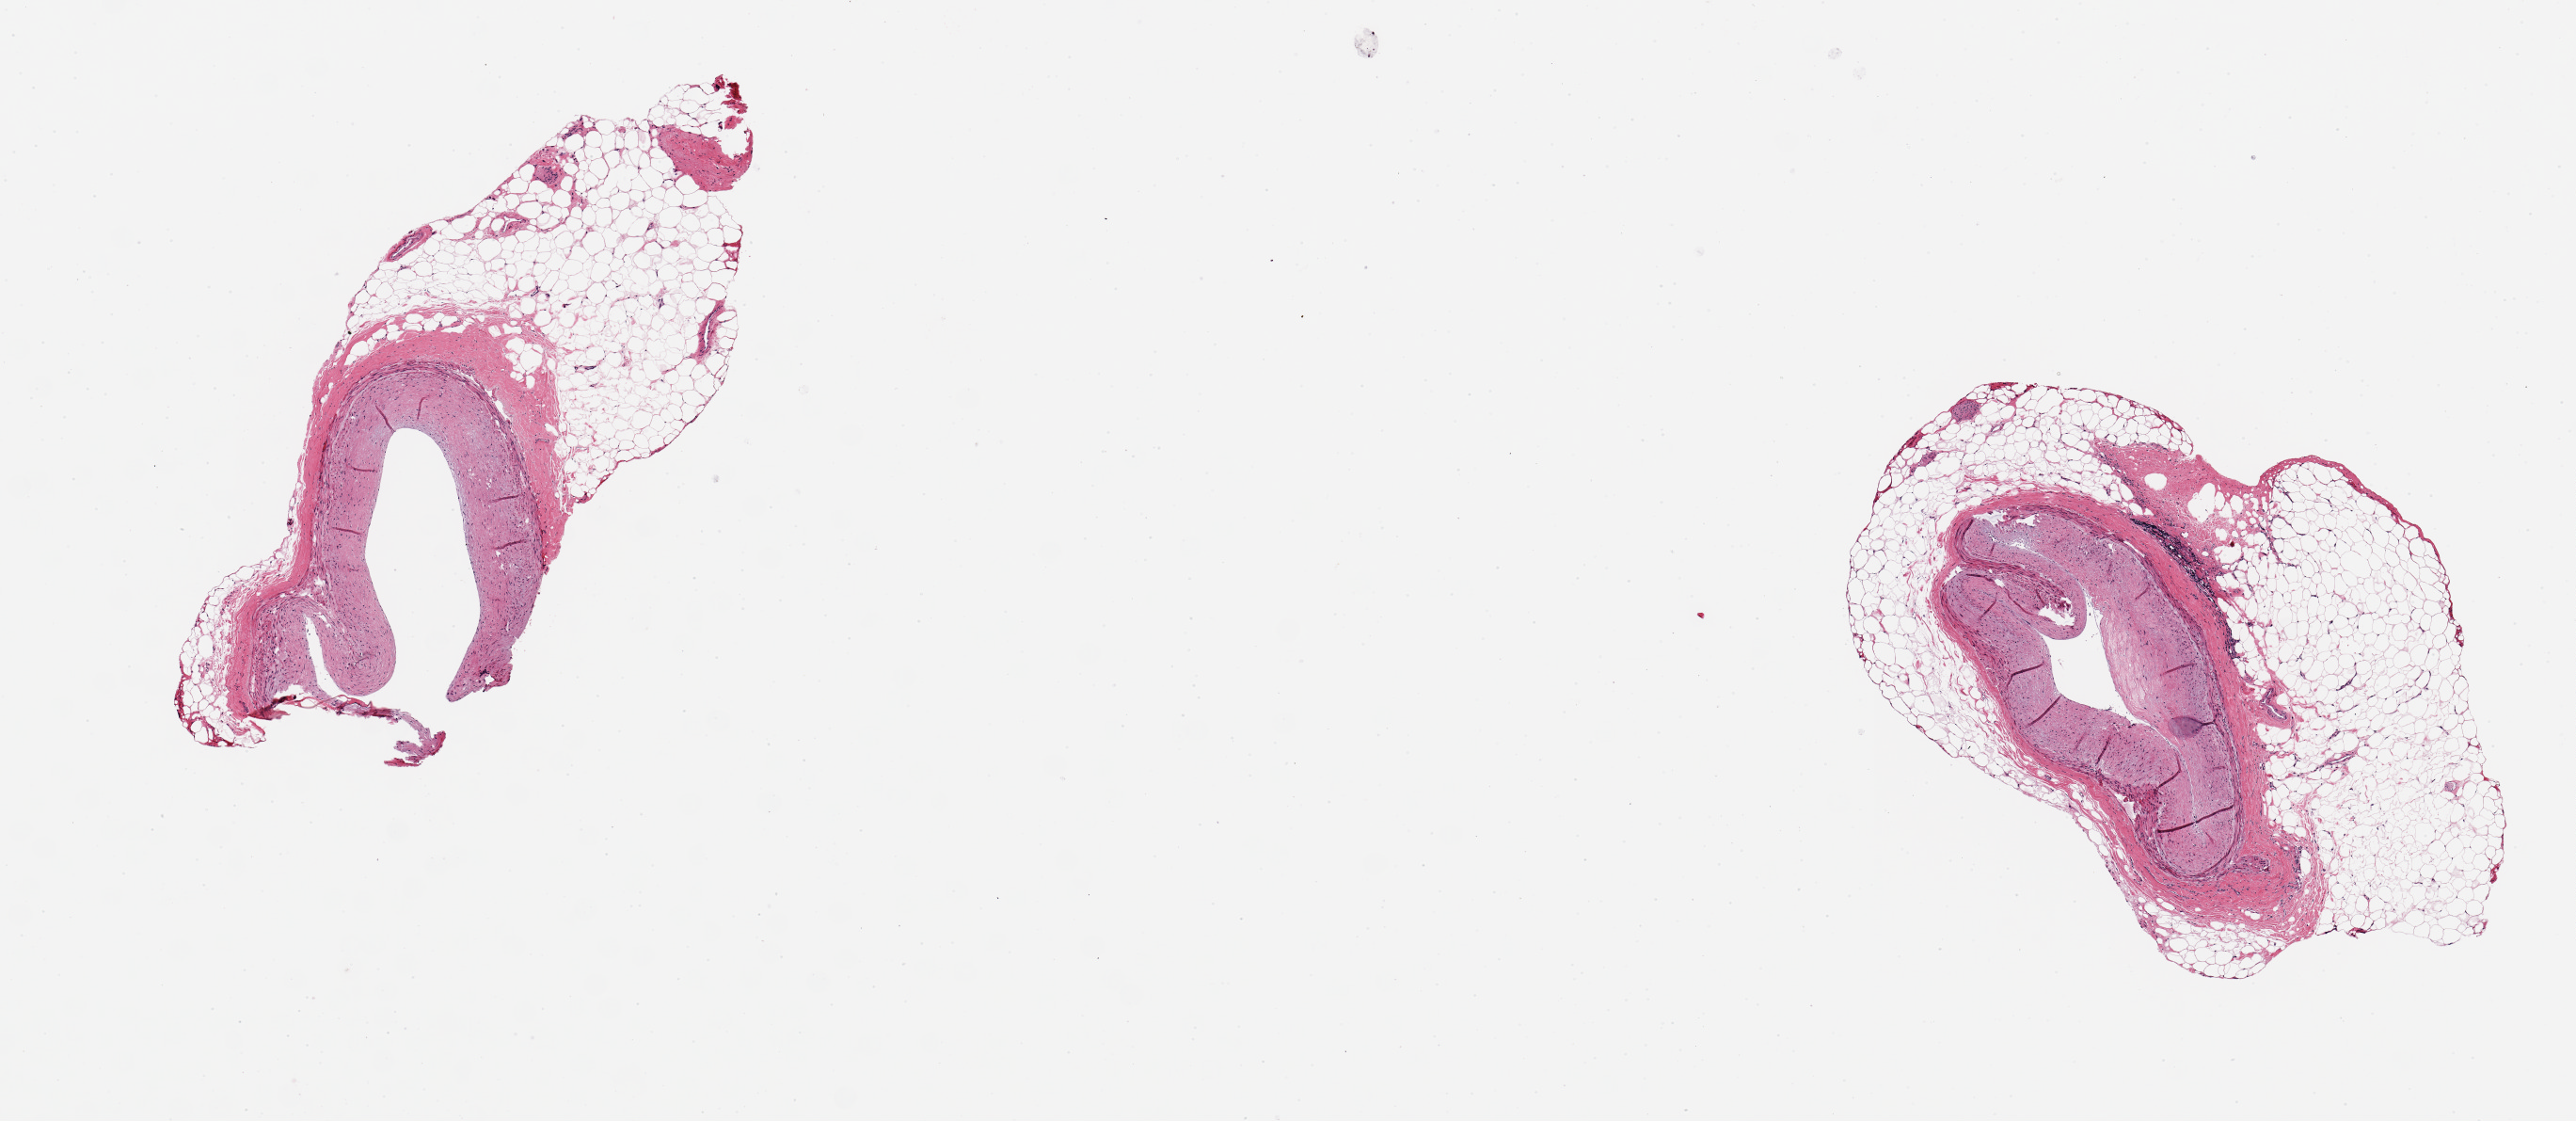
Haematoxylin and eosin whole-slide image — low-resolution overview of the scanned area, about 10.8 x 4.7 mm. PAXgene-fixed paraffin-embedded (PFPE) section. Section of coronary artery (target tissue). Donor tissue sample. Male donor.
Review note (as recorded): 2 pieces 1-2mm arteries with 50% surrounding adipose; small plaque.